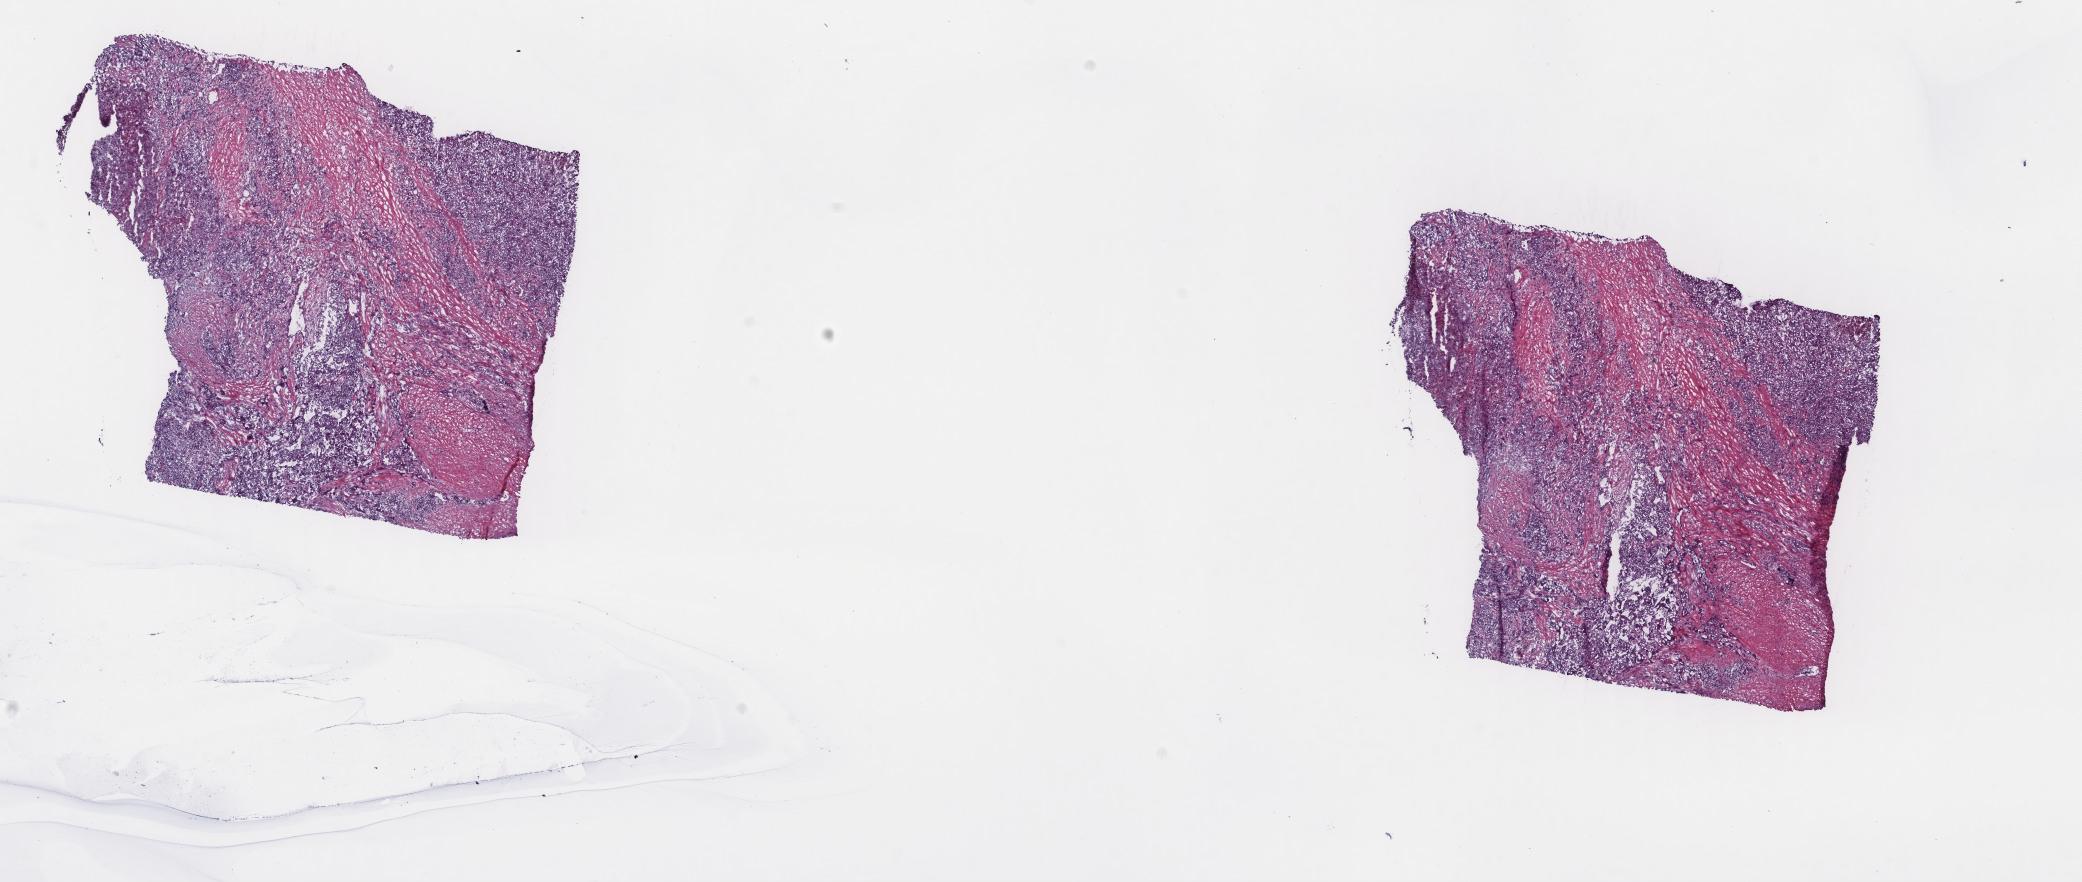
H&E whole-slide image — a low-resolution overview of the entire scanned area, about 16.5 x 7.0 mm; frozen section from the top of the tissue portion; primary tumour sample from the liver. Male, age 50 years at initial diagnosis. Histologic grade: G3 (poorly differentiated). Slide review estimates, as recorded: tumour cells 60%, tumour nuclei 60%, normal cells 0%, stromal cells 40%, necrosis 0%. Infiltration values recorded for this section: lymphocyte infiltration 15%, monocyte infiltration 0%, neutrophil infiltration 0%.
* diagnosis: Hepatocellular carcinoma, NOS
* AJCC pathologic stage: IIIA (6th edition)